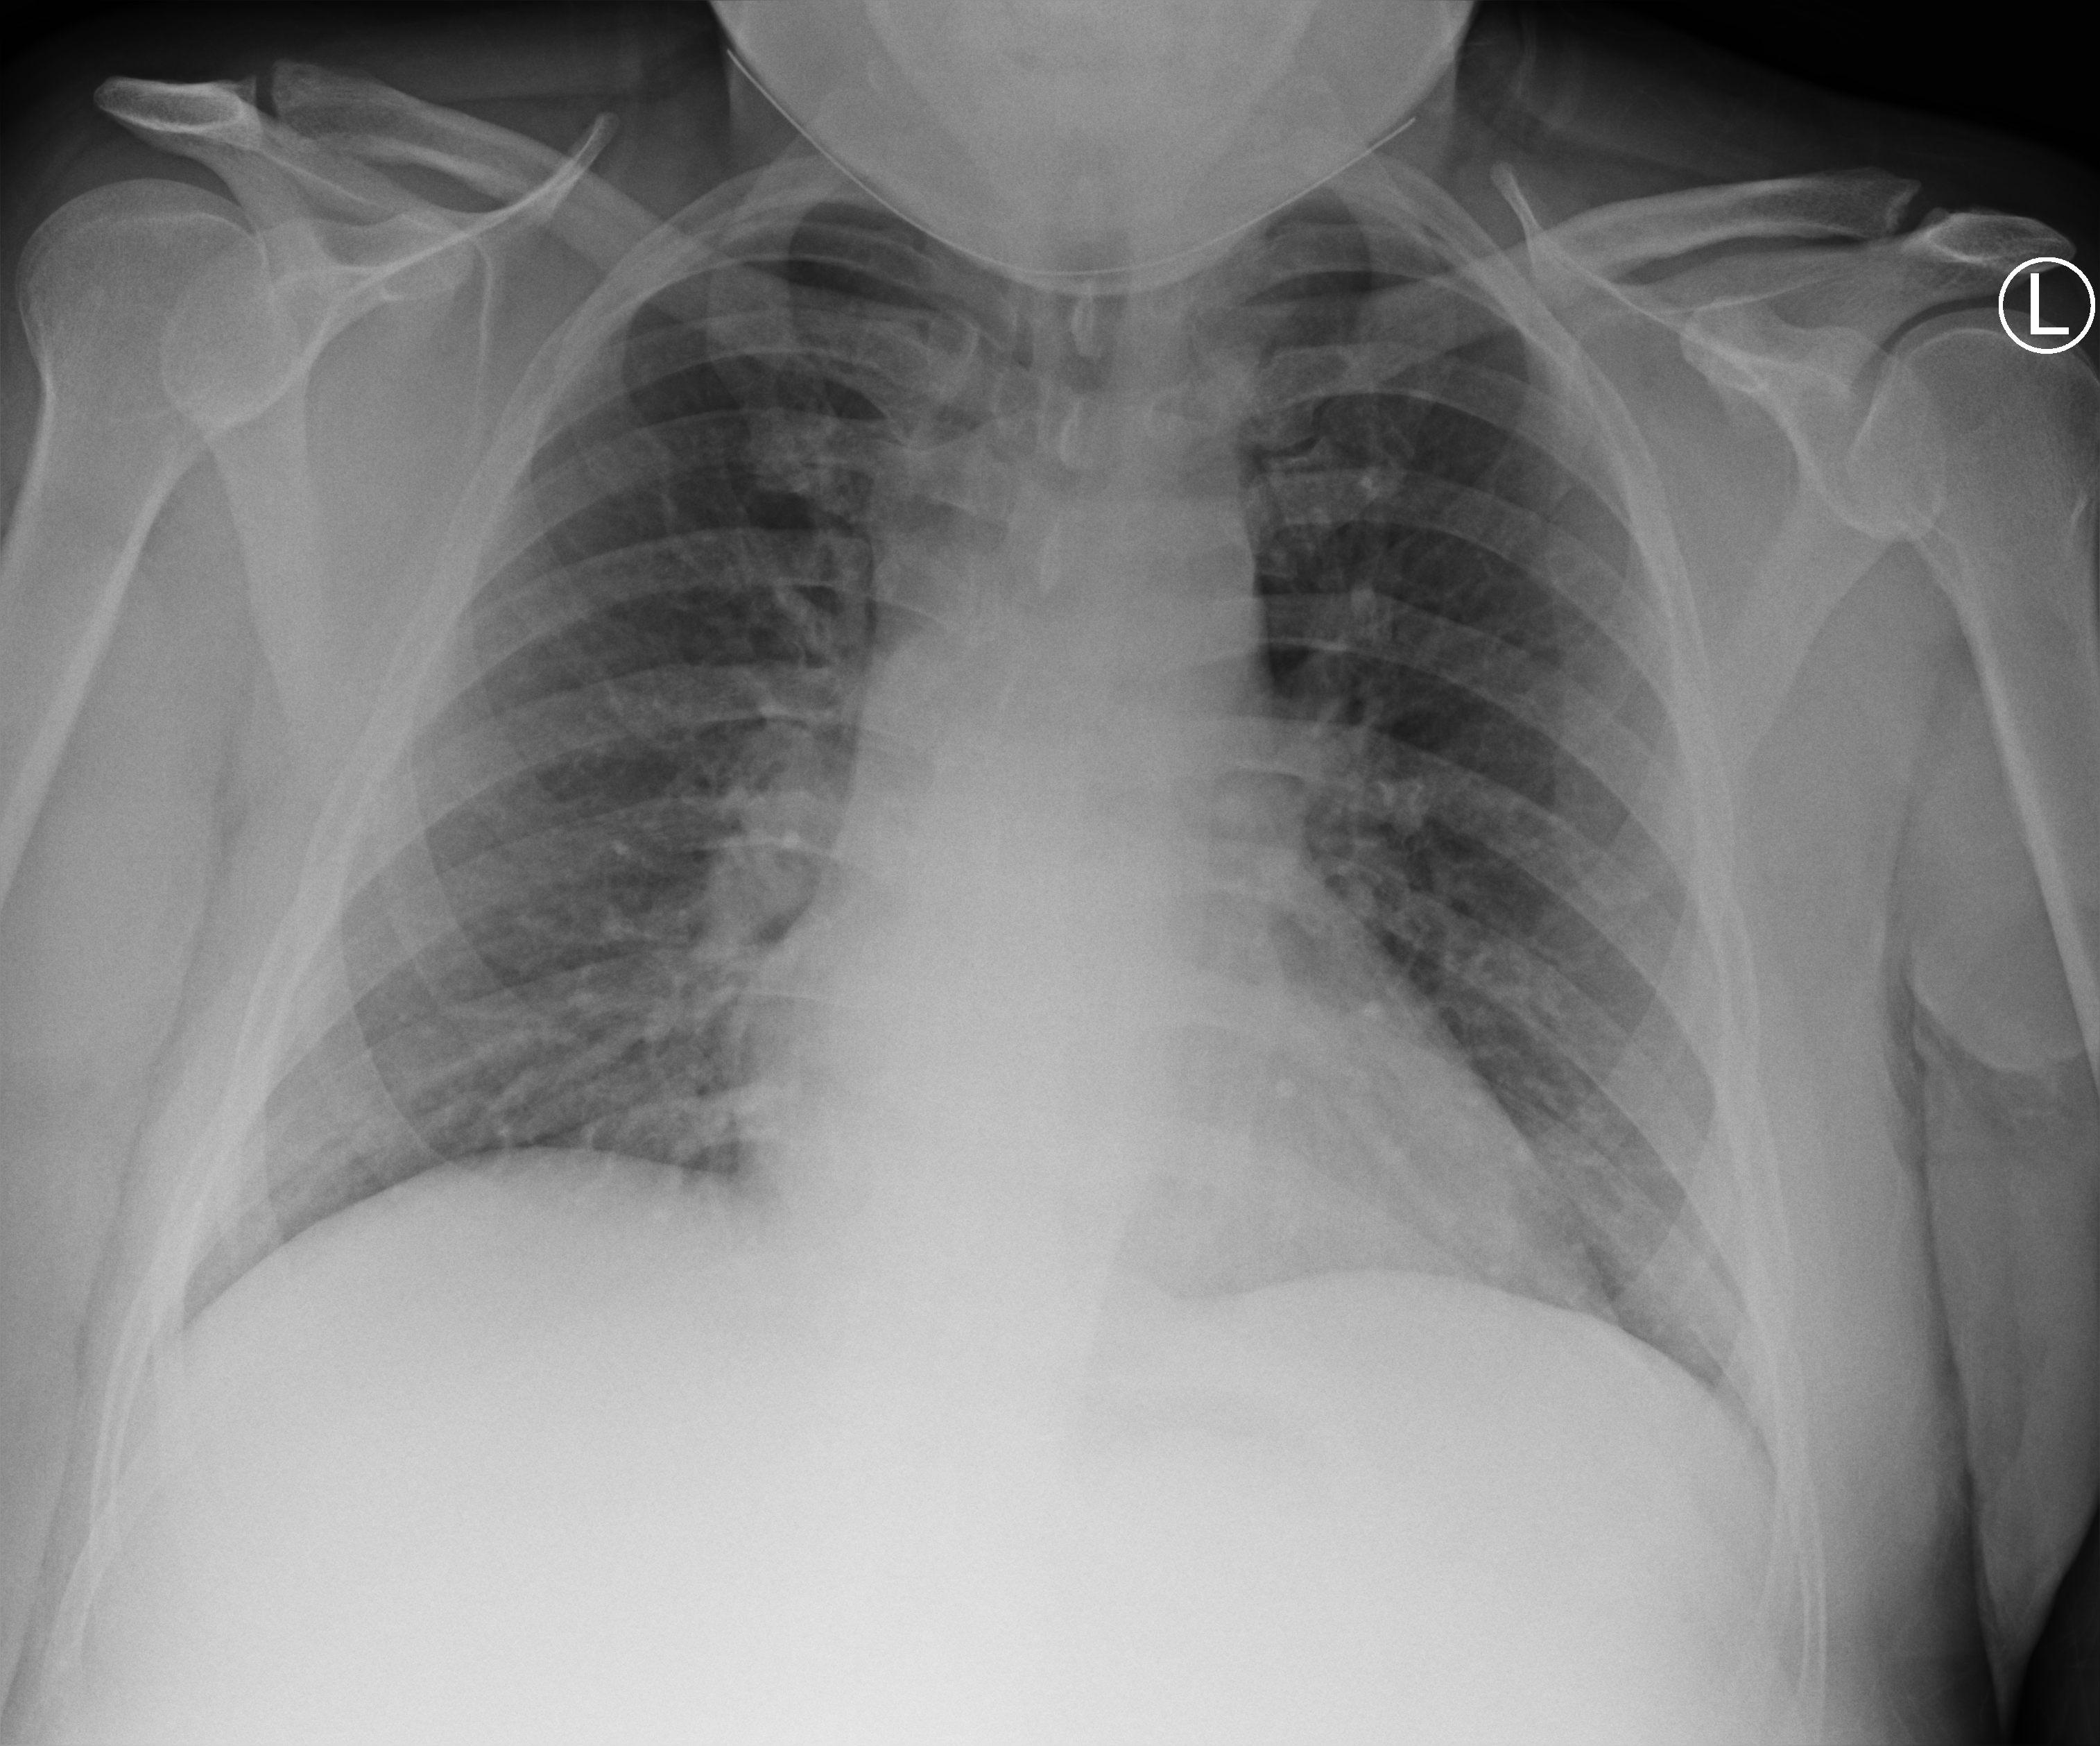
Portable chest radiograph; anteroposterior (AP) projection. Male patient hospitalised with COVID-19, age 18–59 years.
From the hospital-stay record, not from the radiograph (when in the stay this image was taken is not recorded): mechanically ventilated during this hospital stay: no; hypertension (admission record): yes; admitted to intensive care during this hospital stay: no.